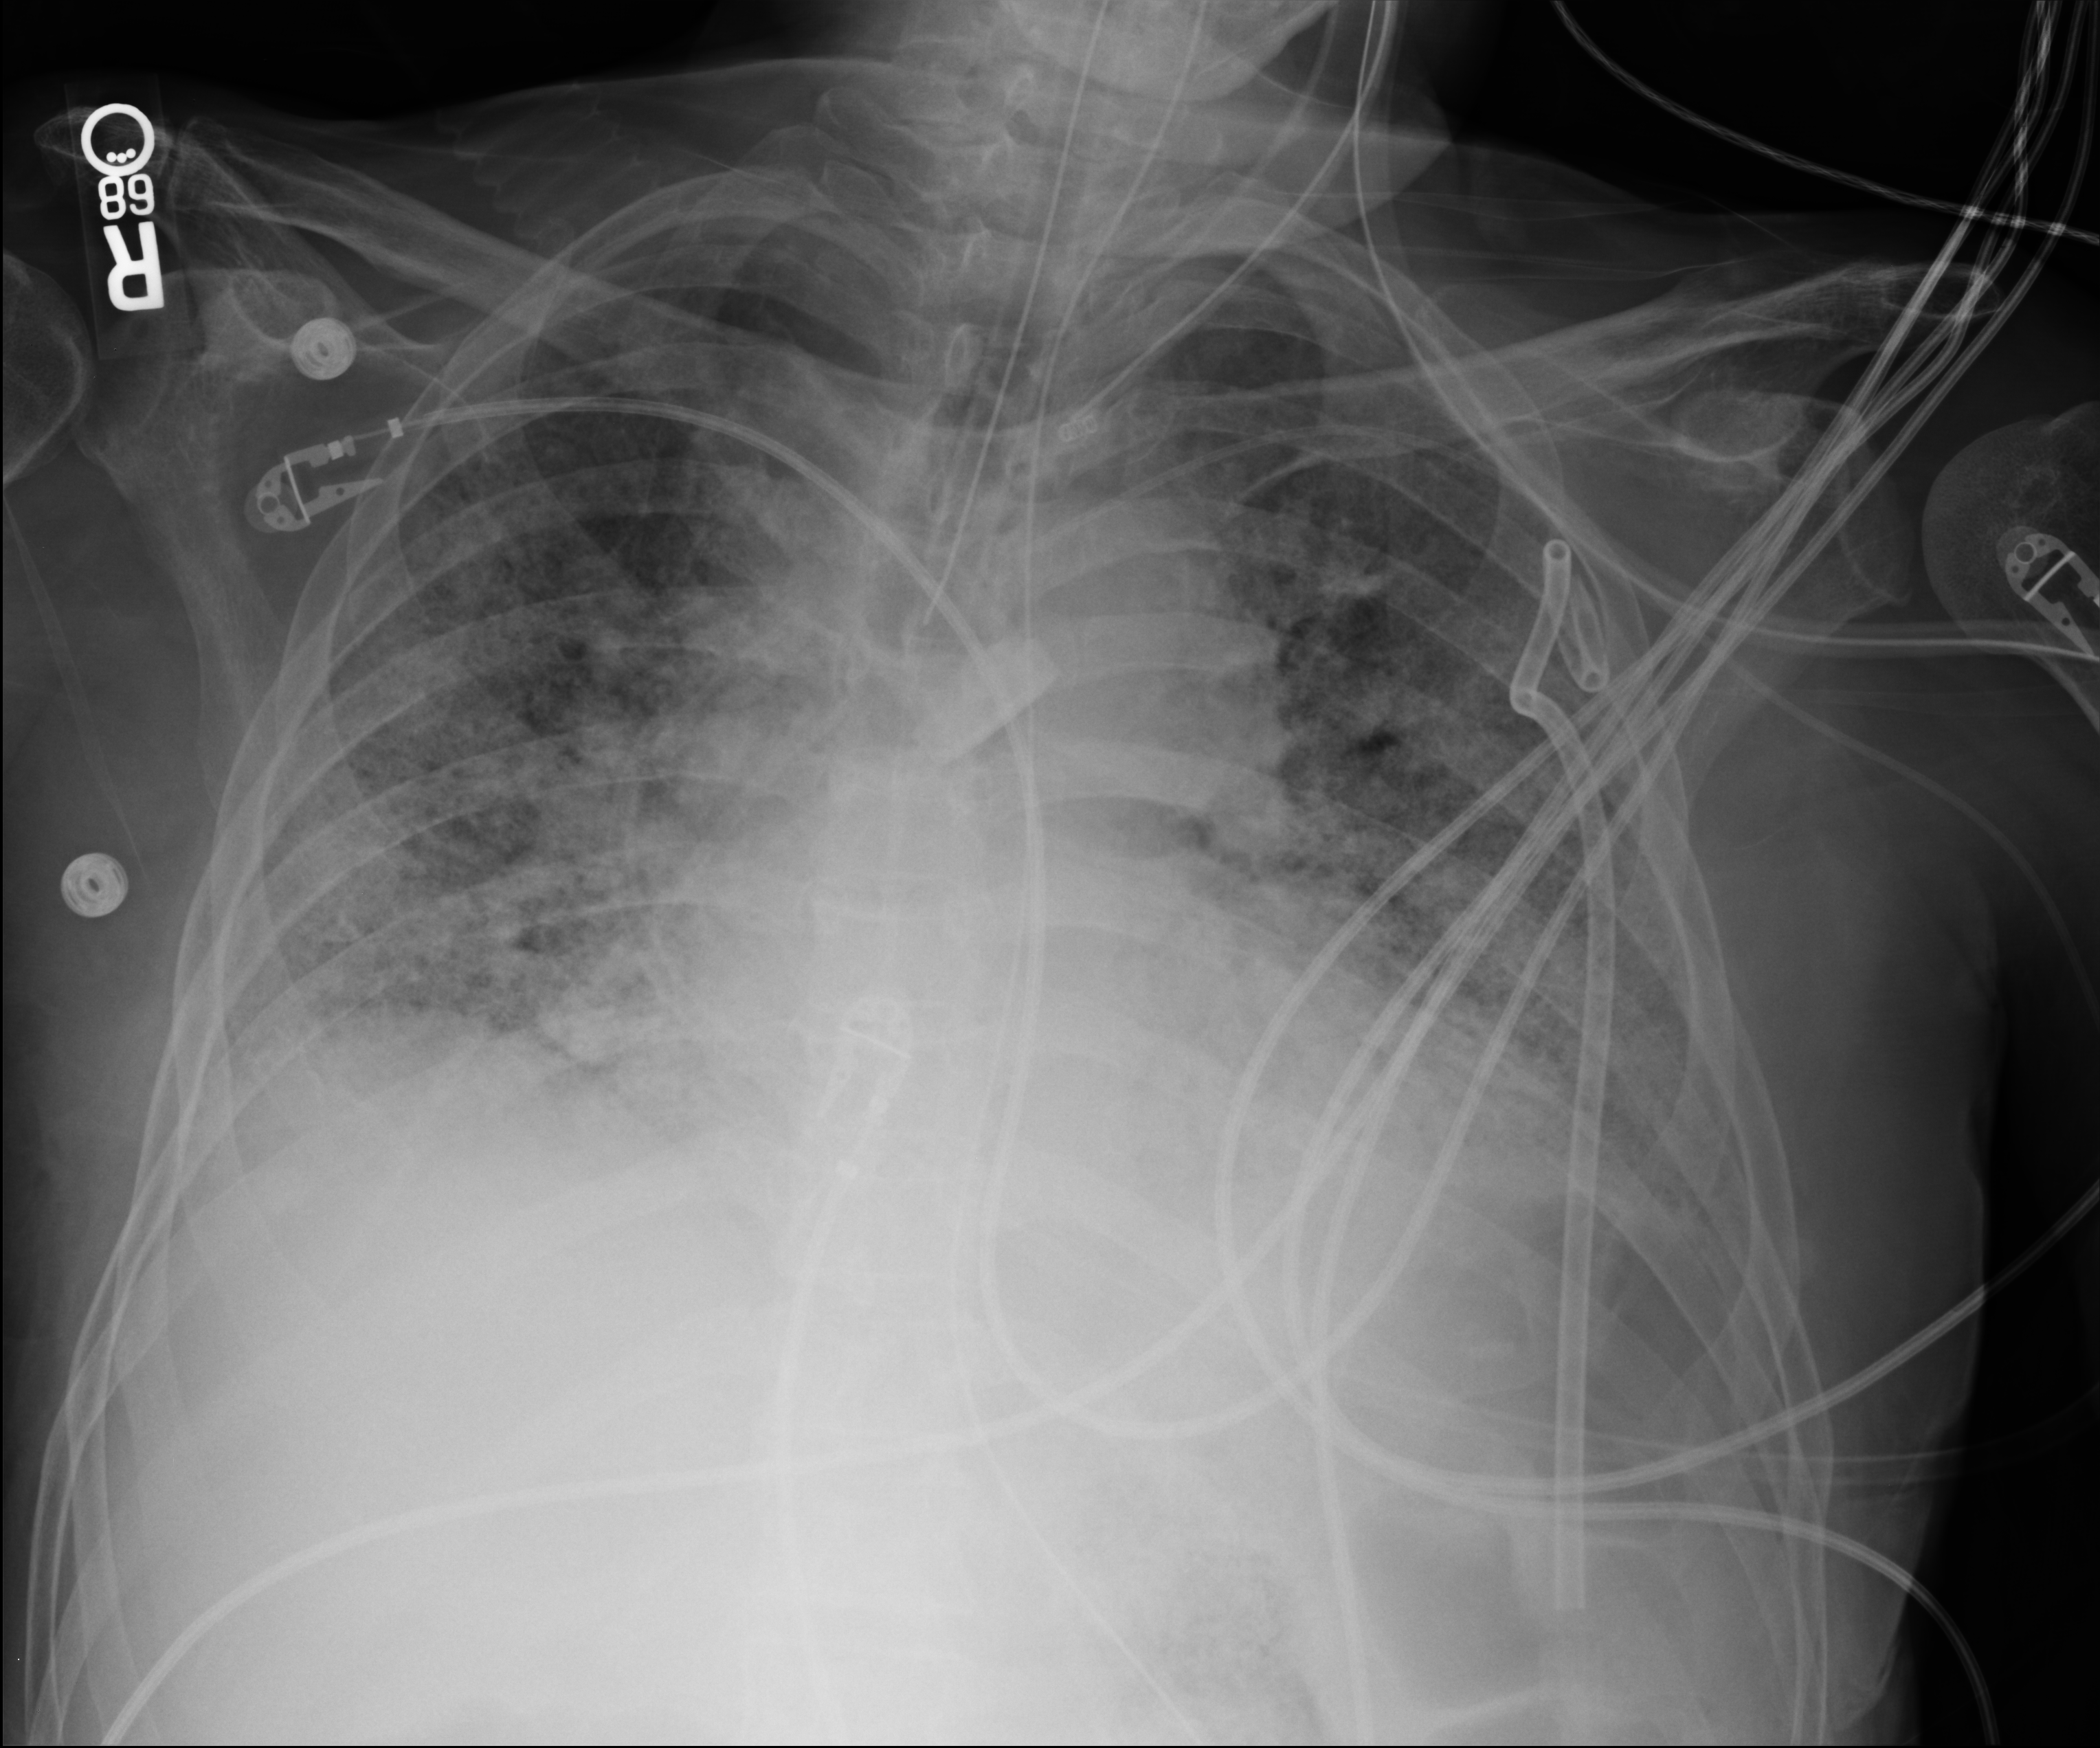
Bedside chest radiograph (computed radiography); anteroposterior (AP) projection. Male patient hospitalised with COVID-19, age 60–74 years.
From the hospital-stay record, not from the radiograph (when in the stay this image was taken is not recorded): mechanically ventilated during this hospital stay: yes.